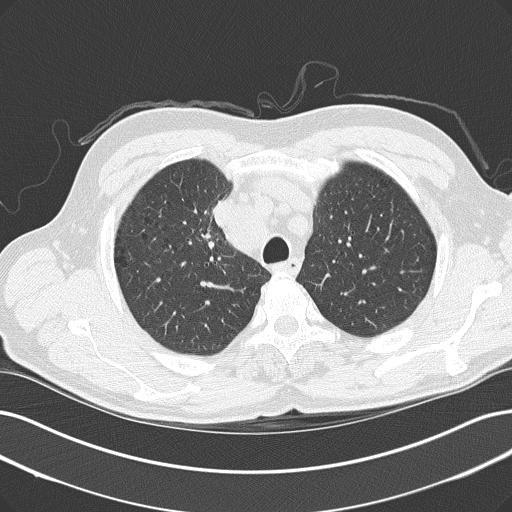
Axial slice from a low-dose chest CT screening exam; baseline annual screen; lung window (W 1500 / L -600 HU). Male participant, aged 61 years at enrolment. Current smoker at enrolment.
- Expert-annotated lung lesion, bounding box <187,215,246,264> (left, top, right, bottom; pixels).
- The screening reader recorded 2 non-calcified nodules or masses ≥4 mm on this exam (right upper lobe, right upper lobe); which of them this box marks is not recorded.
- Official screen result: positive, change unspecified: nodule(s) >= 4 mm or enlarging nodule(s), mass(es), or other non-specific abnormalities suspicious for lung cancer.